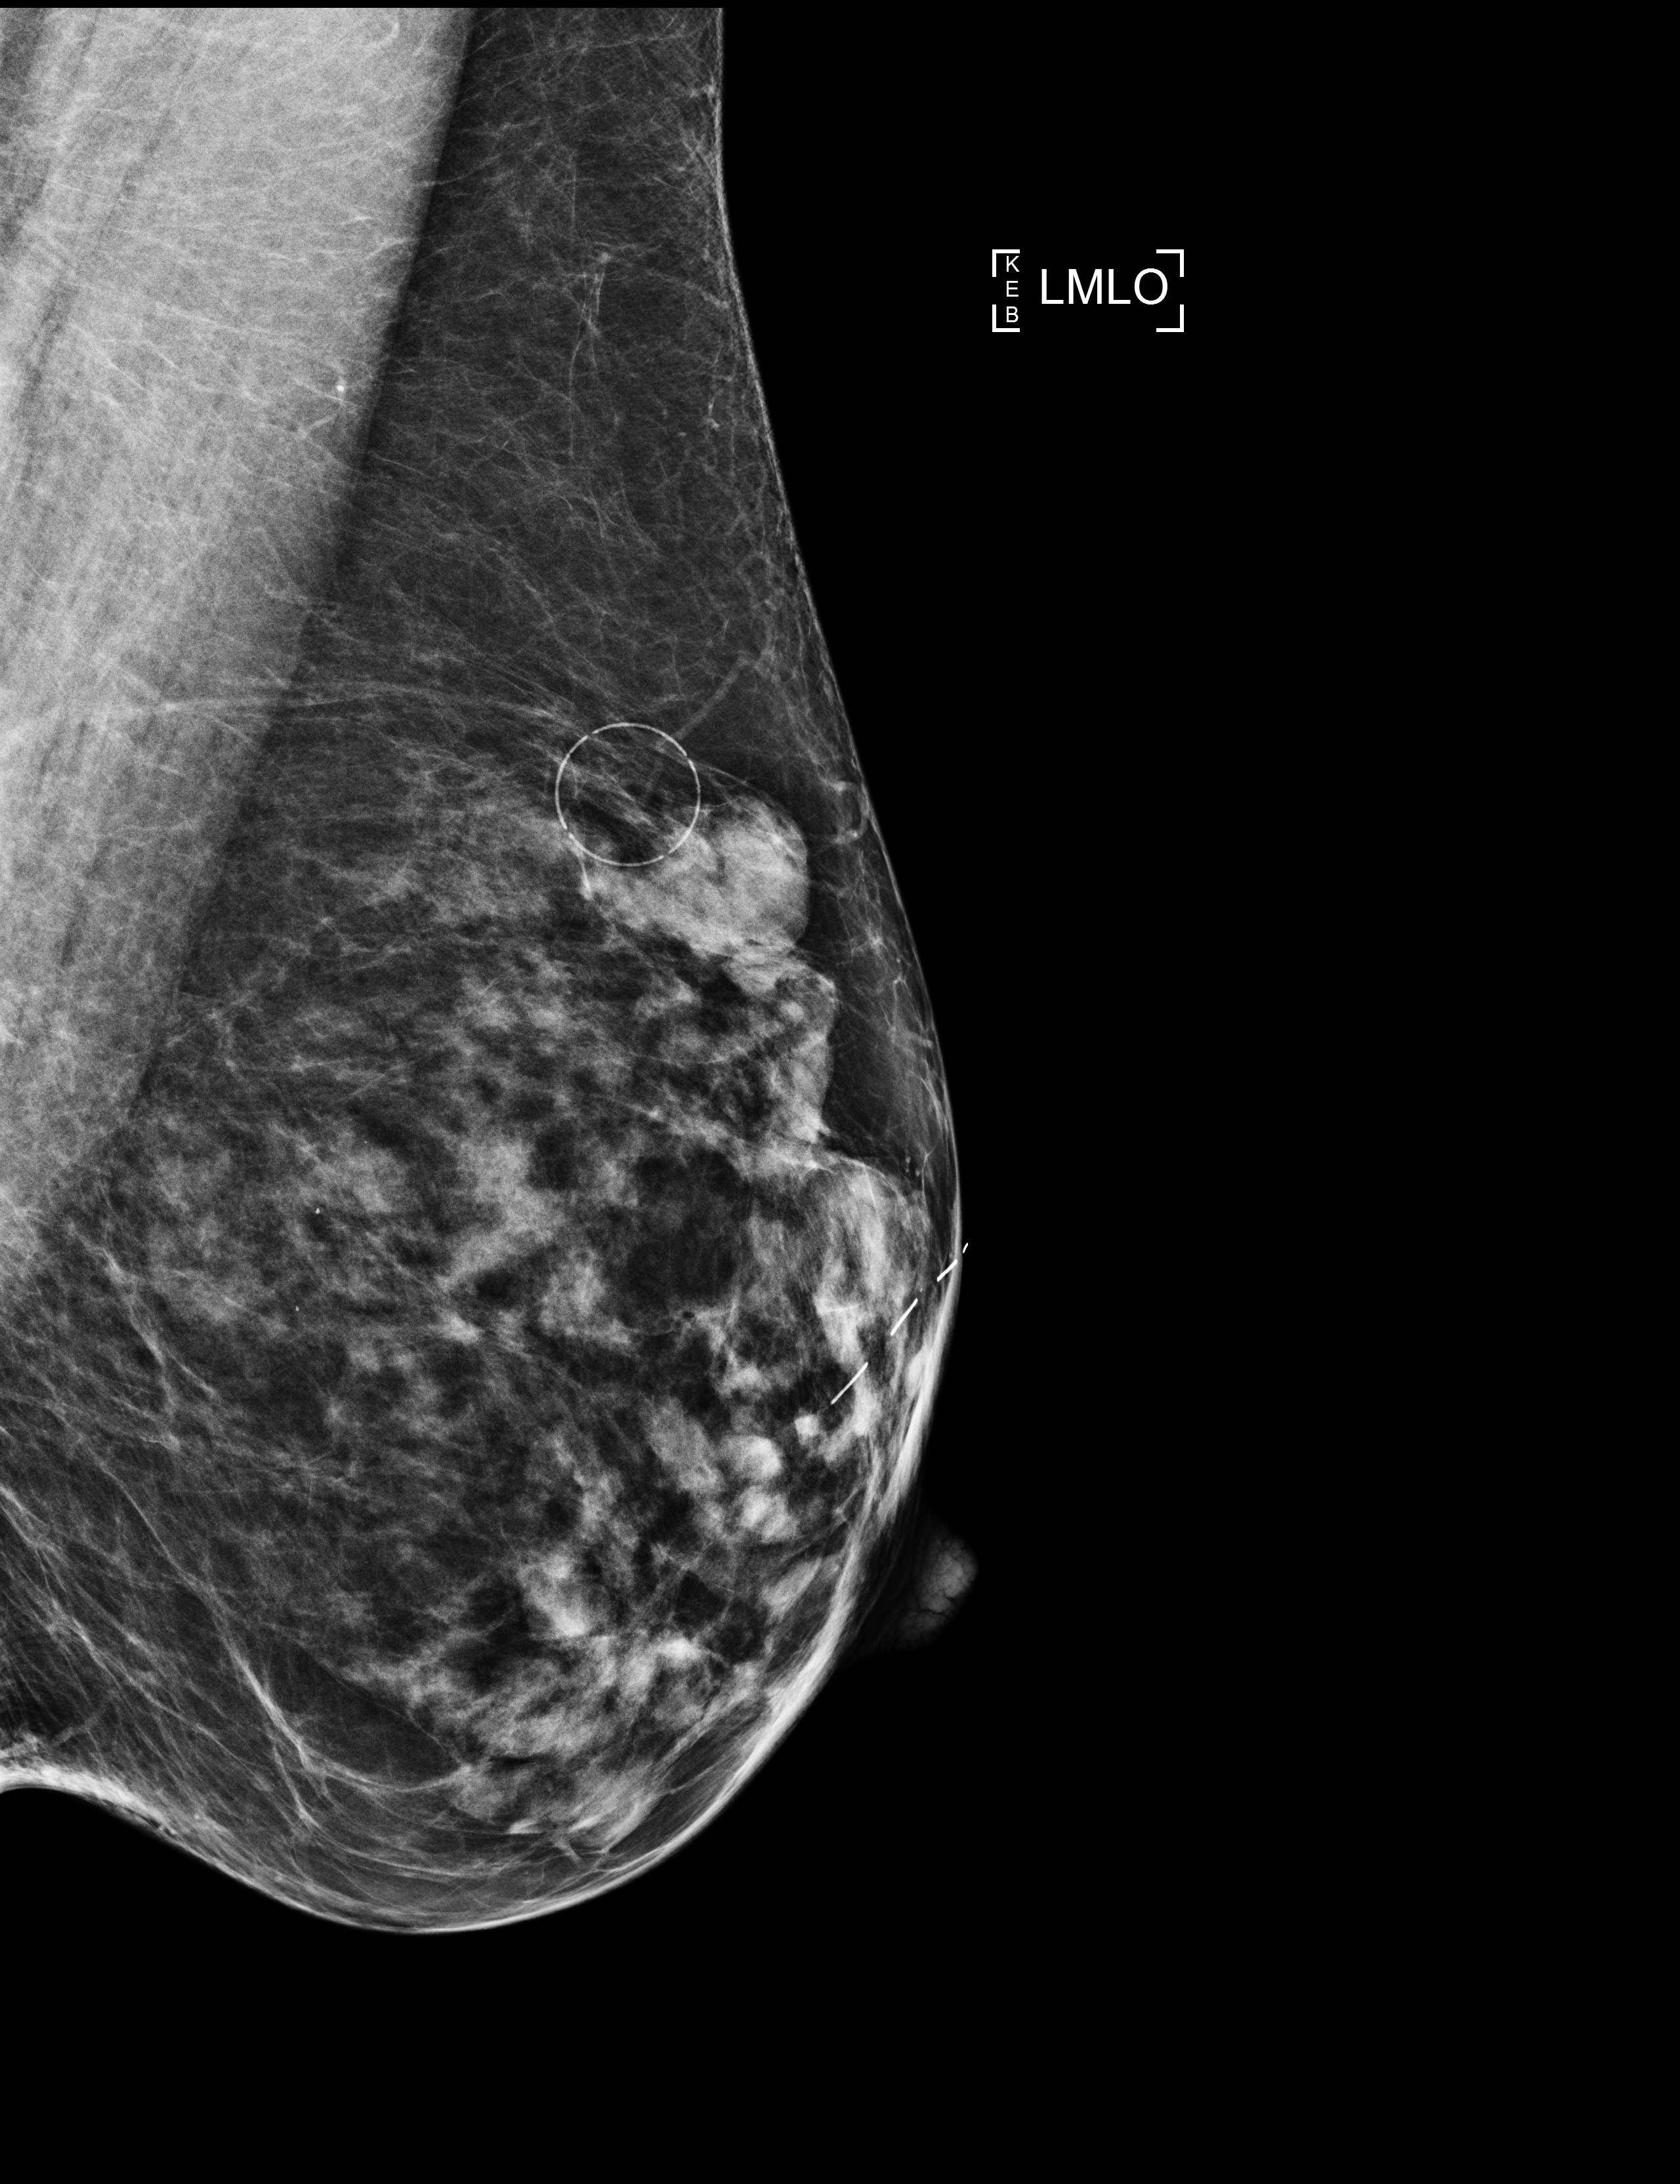
Screening examination. Female patient, age 73 years.
Image type: full-field digital mammogram. Breast: left. Projection: medio-lateral oblique projection.